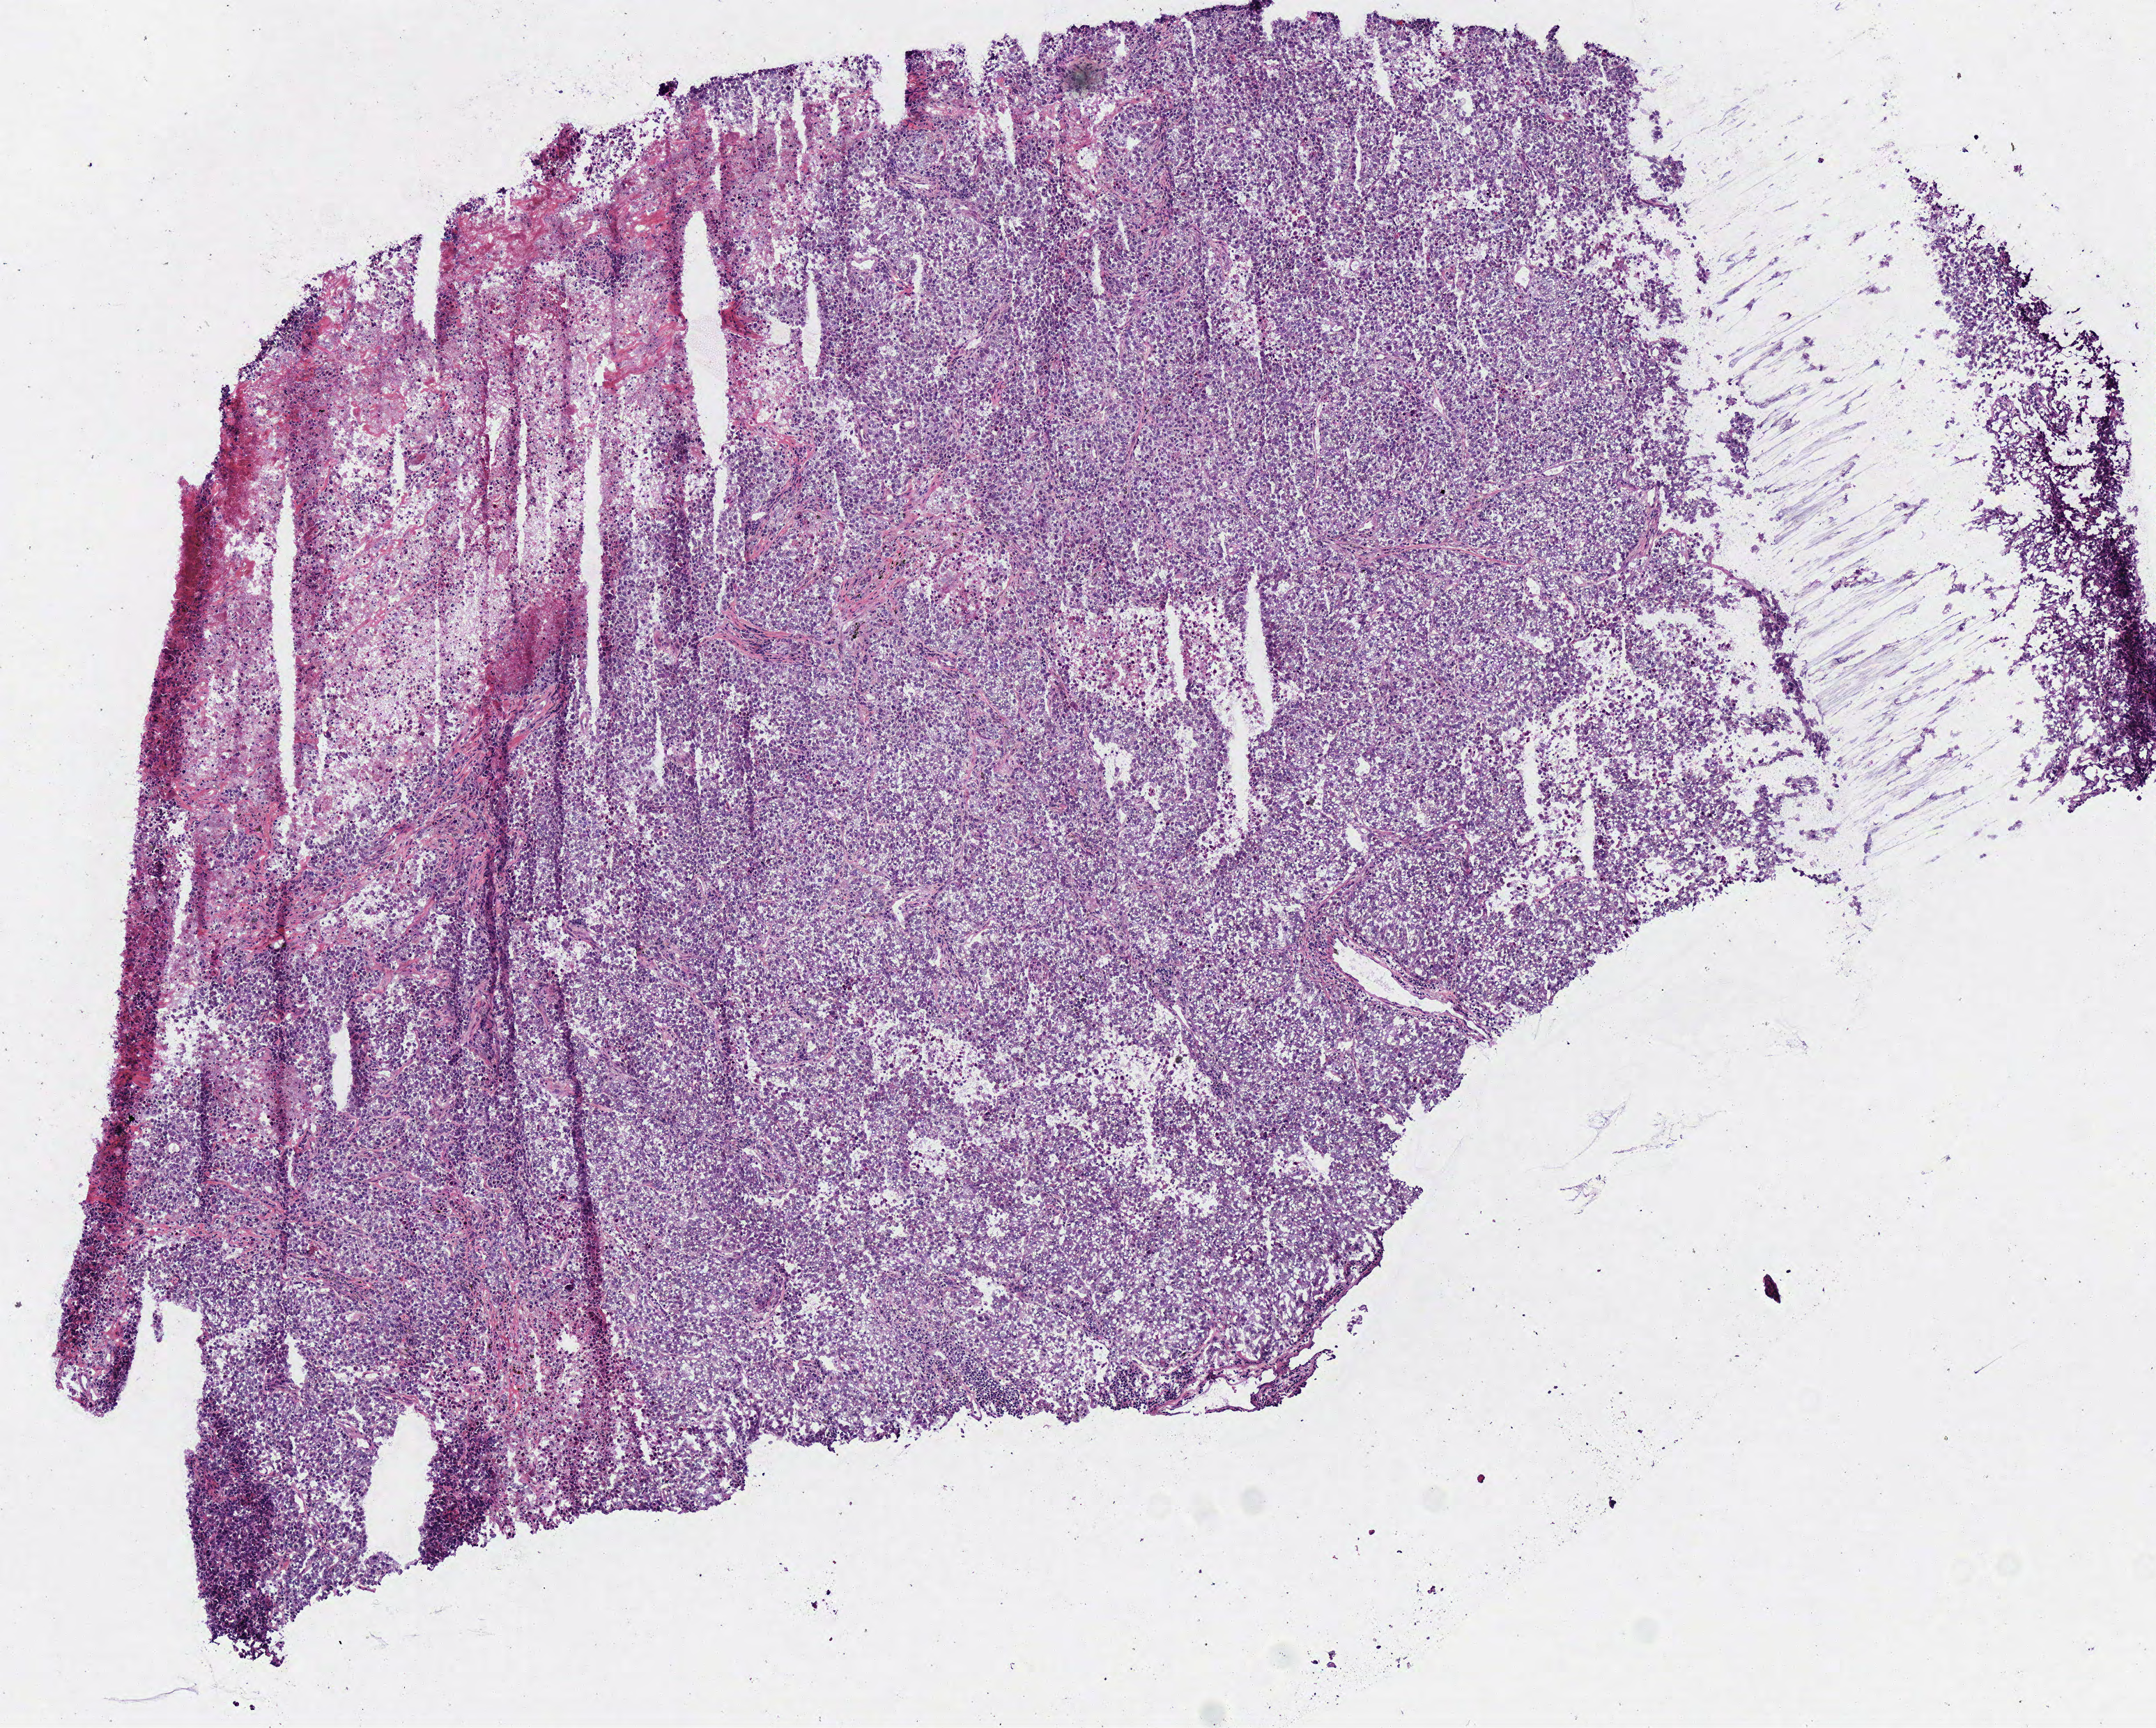
H&E-stained whole-slide image — shown as a low-resolution overview of the whole scanned area (about 6.1 x 4.9 mm, acquisition: 40x scan); frozen section; lung, primary tumour sample. Patient: female, age at initial diagnosis 52 years. Composition of this section per pathologist review: tumour cells 85%, tumour nuclei 85%, normal cells 0%, stromal cells 0%, necrosis 15%.
AJCC pathologic stage: IB. TNM: T2 N0 MX. Histologic diagnosis: Adenocarcinoma, NOS (upper lobe, lung).